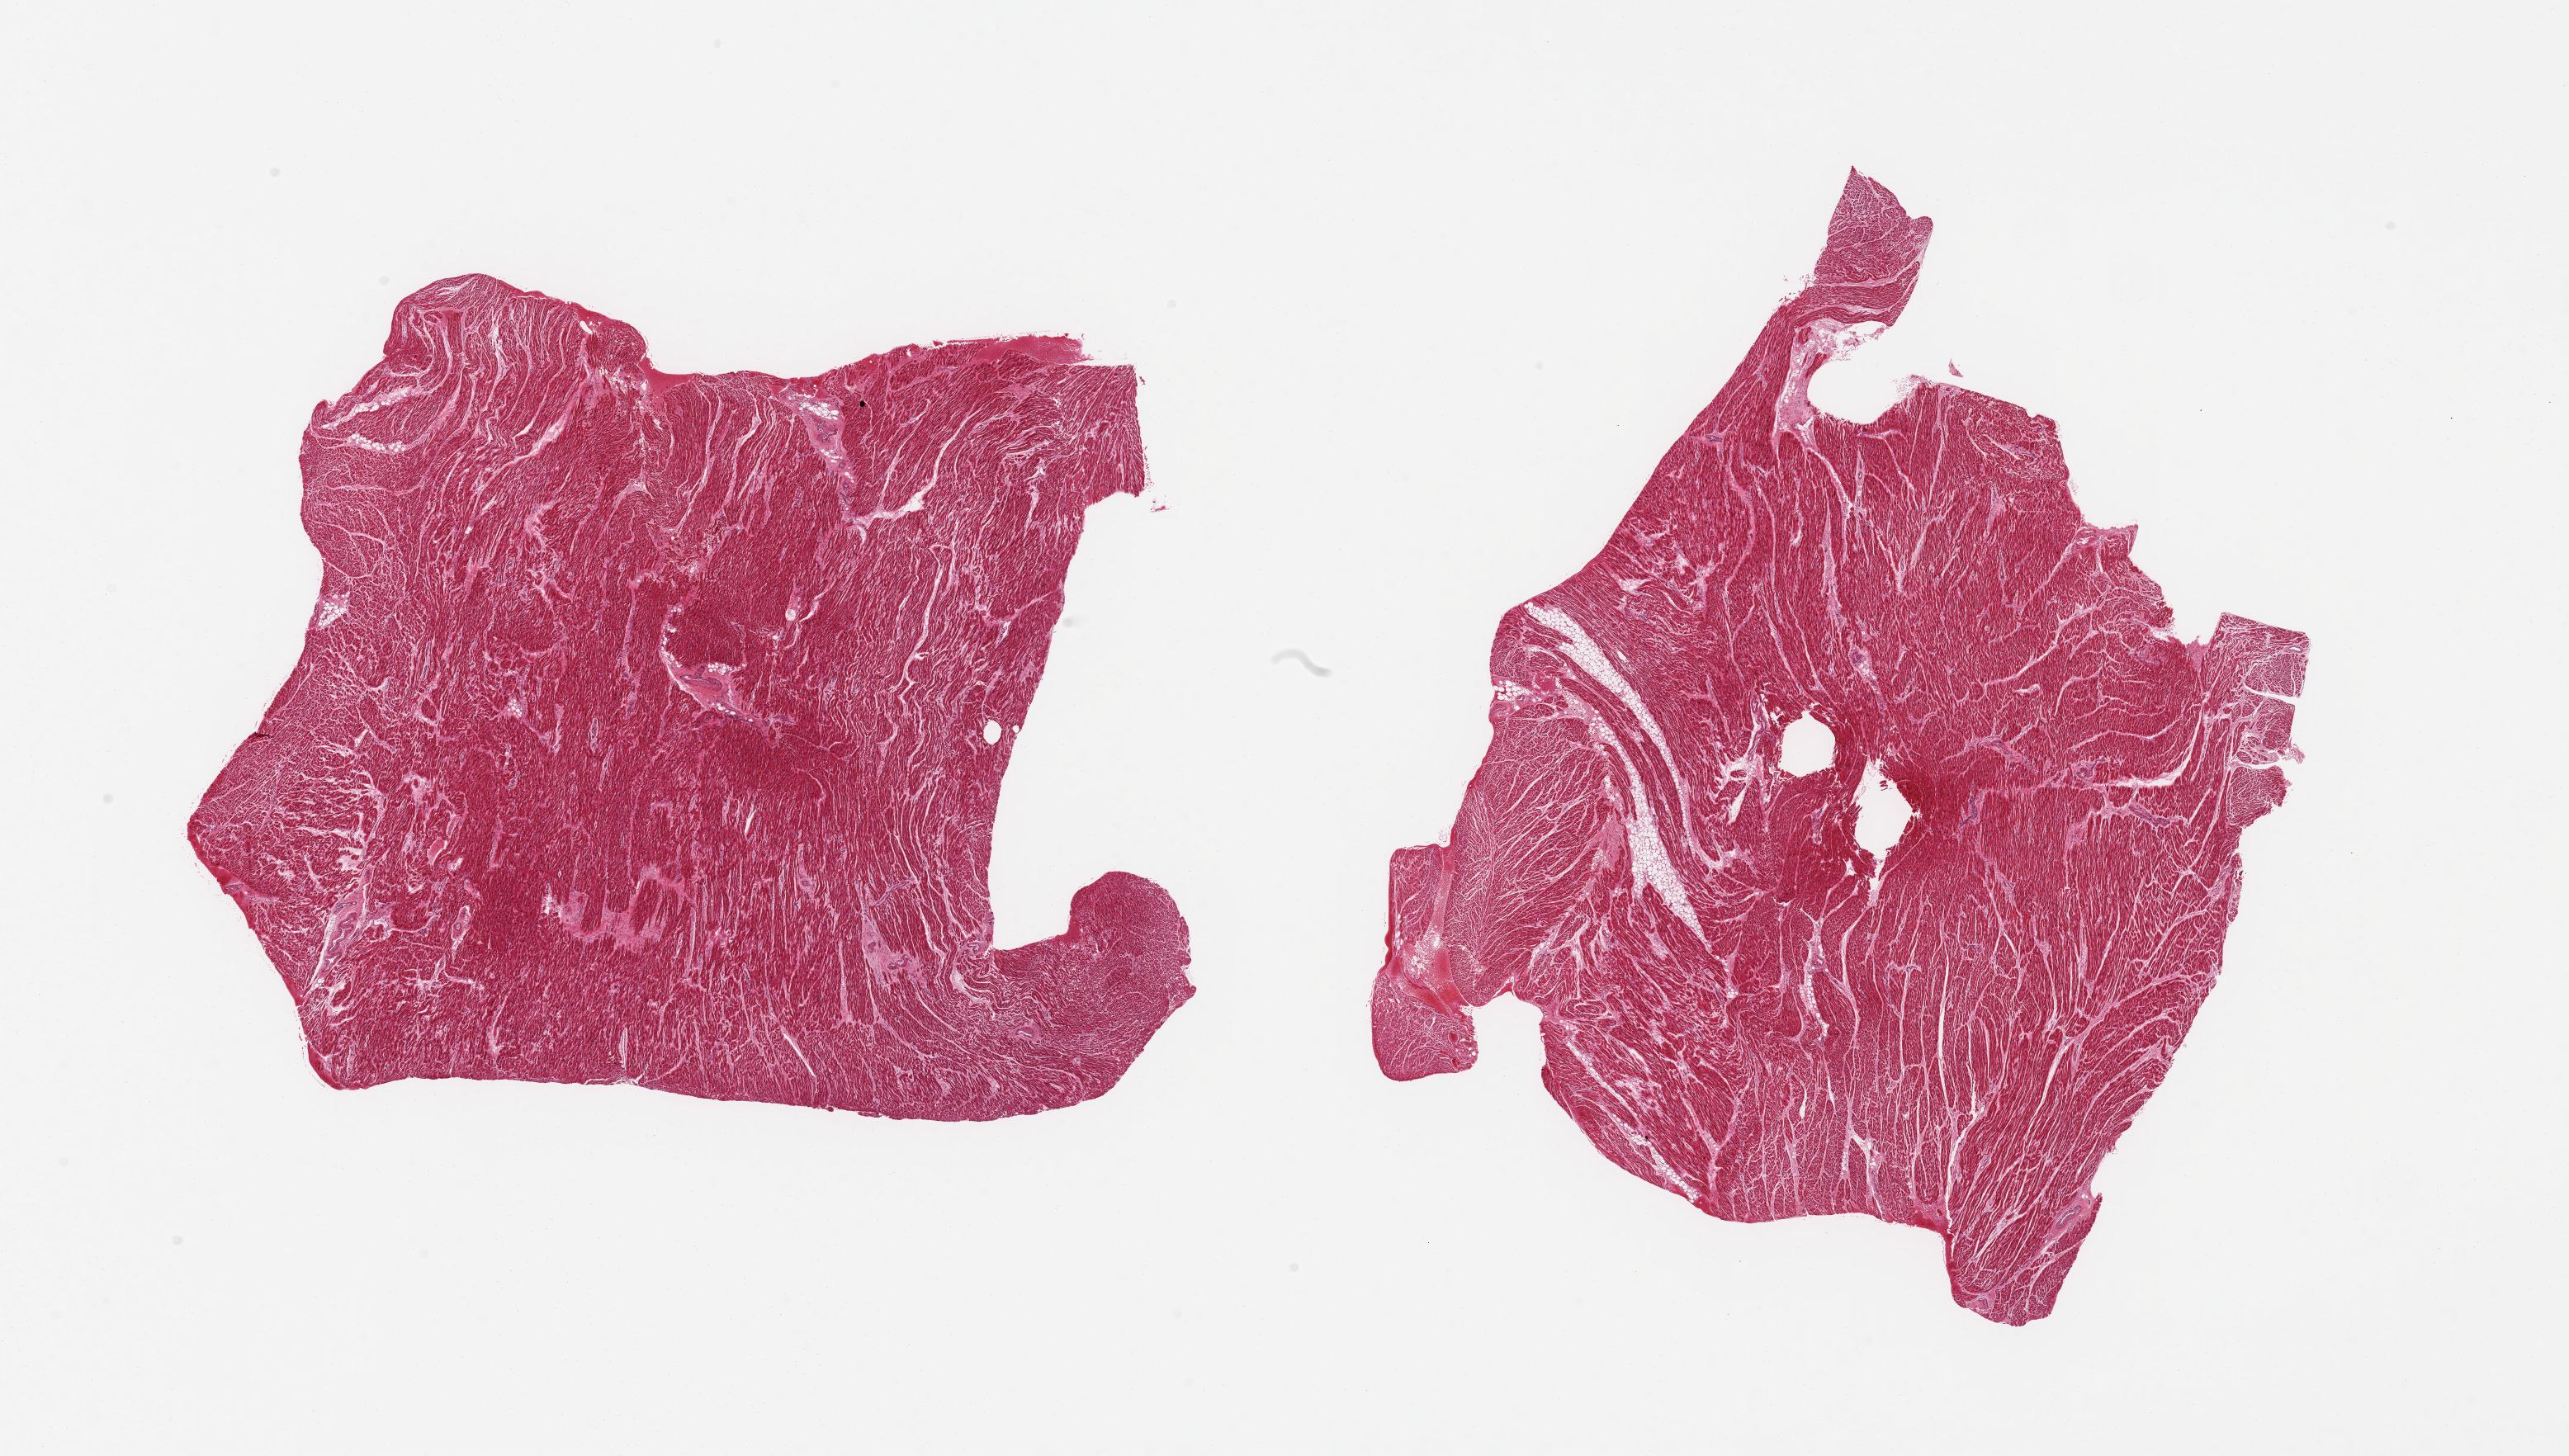
Whole-slide image, haematoxylin and eosin stain, low-resolution overview of the scanned area, about 24.6 x 14.0 mm (acquisition: 20x scan), PAXgene-fixed paraffin-embedded (PFPE) section, target tissue: heart, tissue donor sample.
Review note (as recorded): 2 pieces; no scars; 5% internal fat in 1 piece.